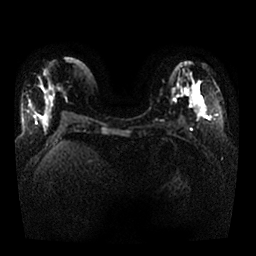
Breast MRI, one axial slice. Slice 13 of 25 in the series (ordered by position). Diffusion-weighted series; image 2 of 4 stored at this slice position (different b-values; order by instance number). 1.5 T. 256 × 256 image matrix, field of view 350 × 350 mm. Female patient.
Structures marked on this image (outlined manually by an expert reader):
- tumour on diffusion-weighted imaging: box from (x=192, y=93) to (x=199, y=101) px